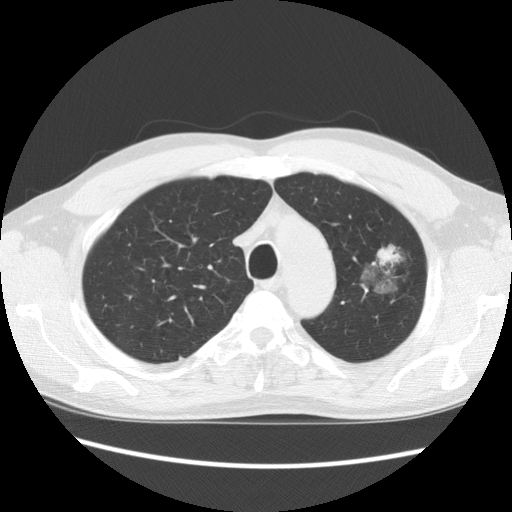
Chest CT (low-dose screening protocol), one axial image; second annual screen; lung window (W 1500 / L -600 HU); 140 kVp; slice 107 of 139 in the series. Male participant, aged 61 years at enrolment. Former smoker at enrolment.
• Expert-annotated lung lesion, bounding box <343,223,426,302> (left, top, right, bottom; pixels).
• Screening reader's record for this exam (one nodule recorded; not confirmed to be the boxed lesion): non-calcified nodule or mass ≥4 mm, left upper lobe, 34 × 32 mm, poorly defined margins, mixed attenuation, pre-existing on the prior screen: yes; interval growth: no.
• Lung cancer was diagnosed 704 days after this screen (after the third annual screen): bronchiolo-alveolar adenocarcinoma, NOS, left upper lobe, well differentiated (G1), stage IB (AJCC 6th edition), 44 mm at pathology.